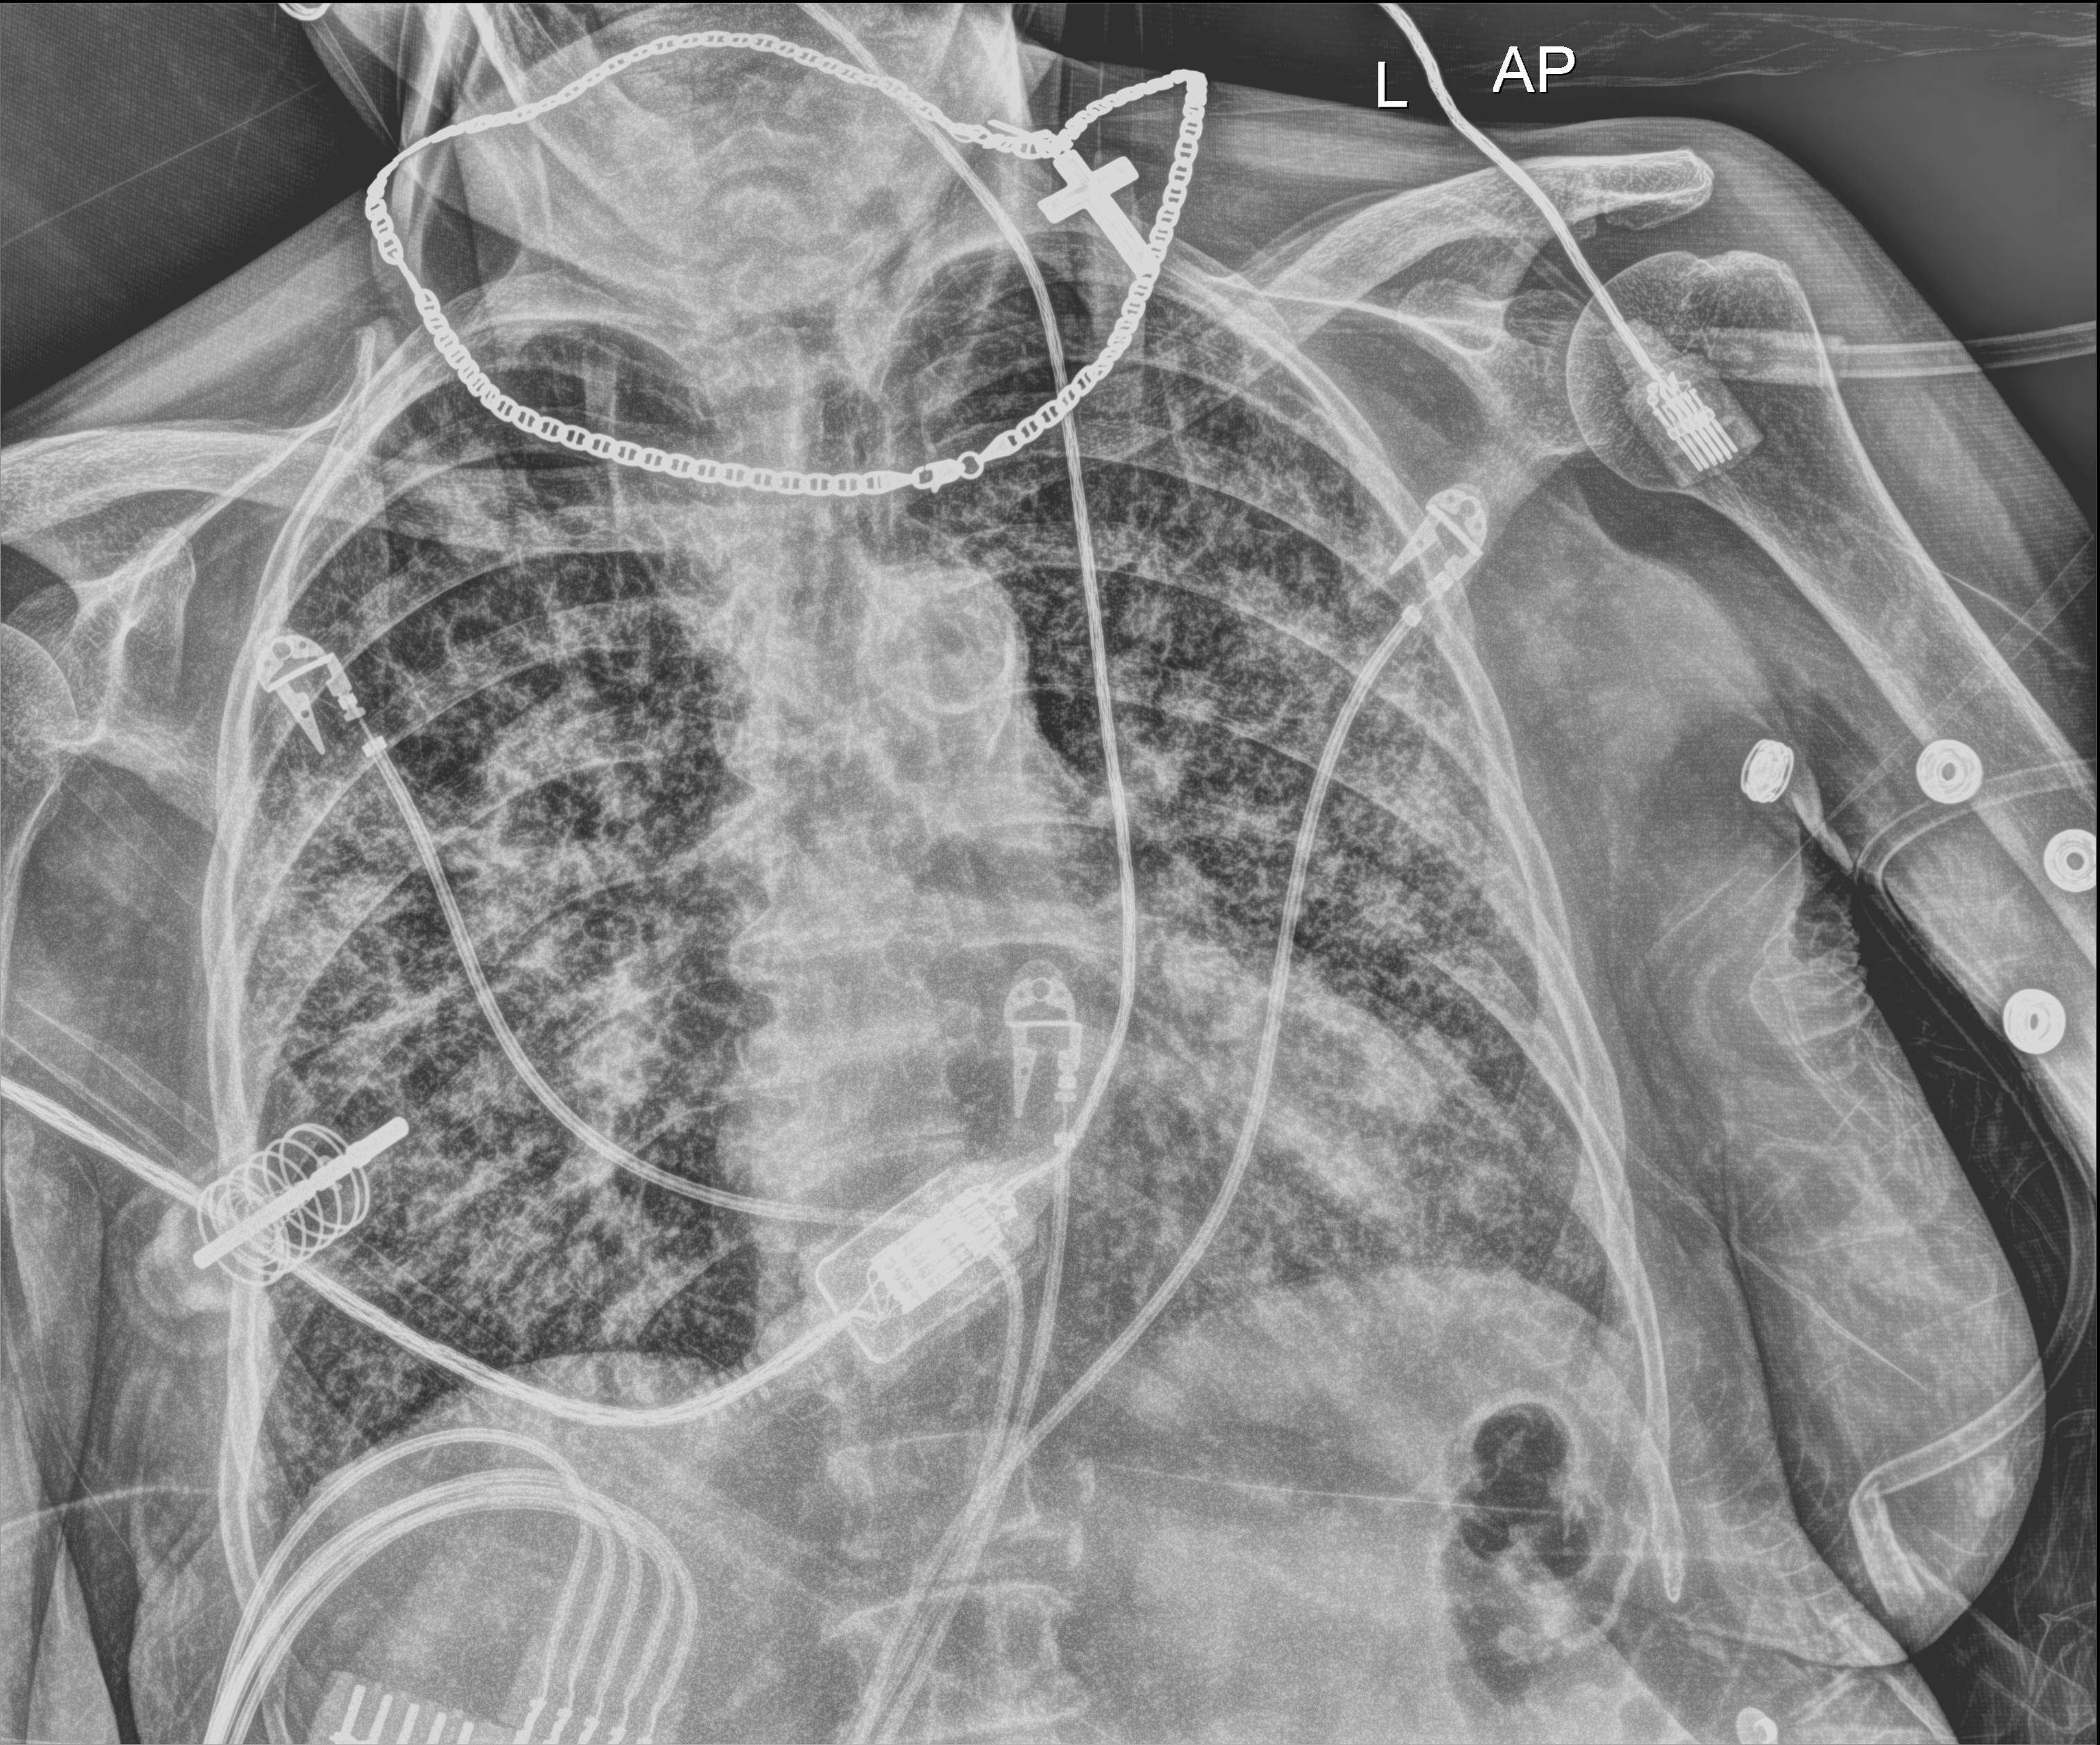
Chest X-ray (portable), anteroposterior (AP) projection. Female patient hospitalised with COVID-19, age 75–90 years.
Hospital-stay facts (about this admission, not read from this image; timing relative to this image not recorded): mechanically ventilated during this hospital stay: no.